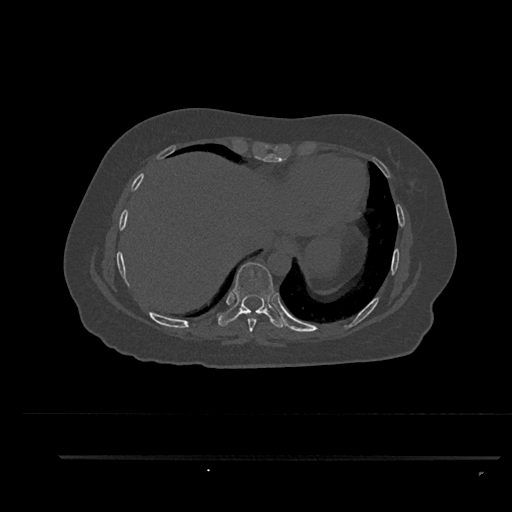
CT including the spine, one axial slice. Slice 428 of 797 in the series (ordered by position). Reconstruction kernel Br40s/3. 120 kVp. Bone window (W 1800 / L 400 HU). 0.5 mm slice thickness. 512 × 512 image matrix, field of view 408 × 408 mm. Patient: female, 44 years. From the clinical record (not read from this slice): primary cancer: renal; vertebrae with lytic lesions (as recorded): L1.
Annotated regions visible in this slice (semi-automatic segmentation, software-assisted and operator-edited):
- T8 vertebra: bounding box <246,310,261,332> (left, top, right, bottom; pixels)
- T9 vertebra: <218,262,285,328>